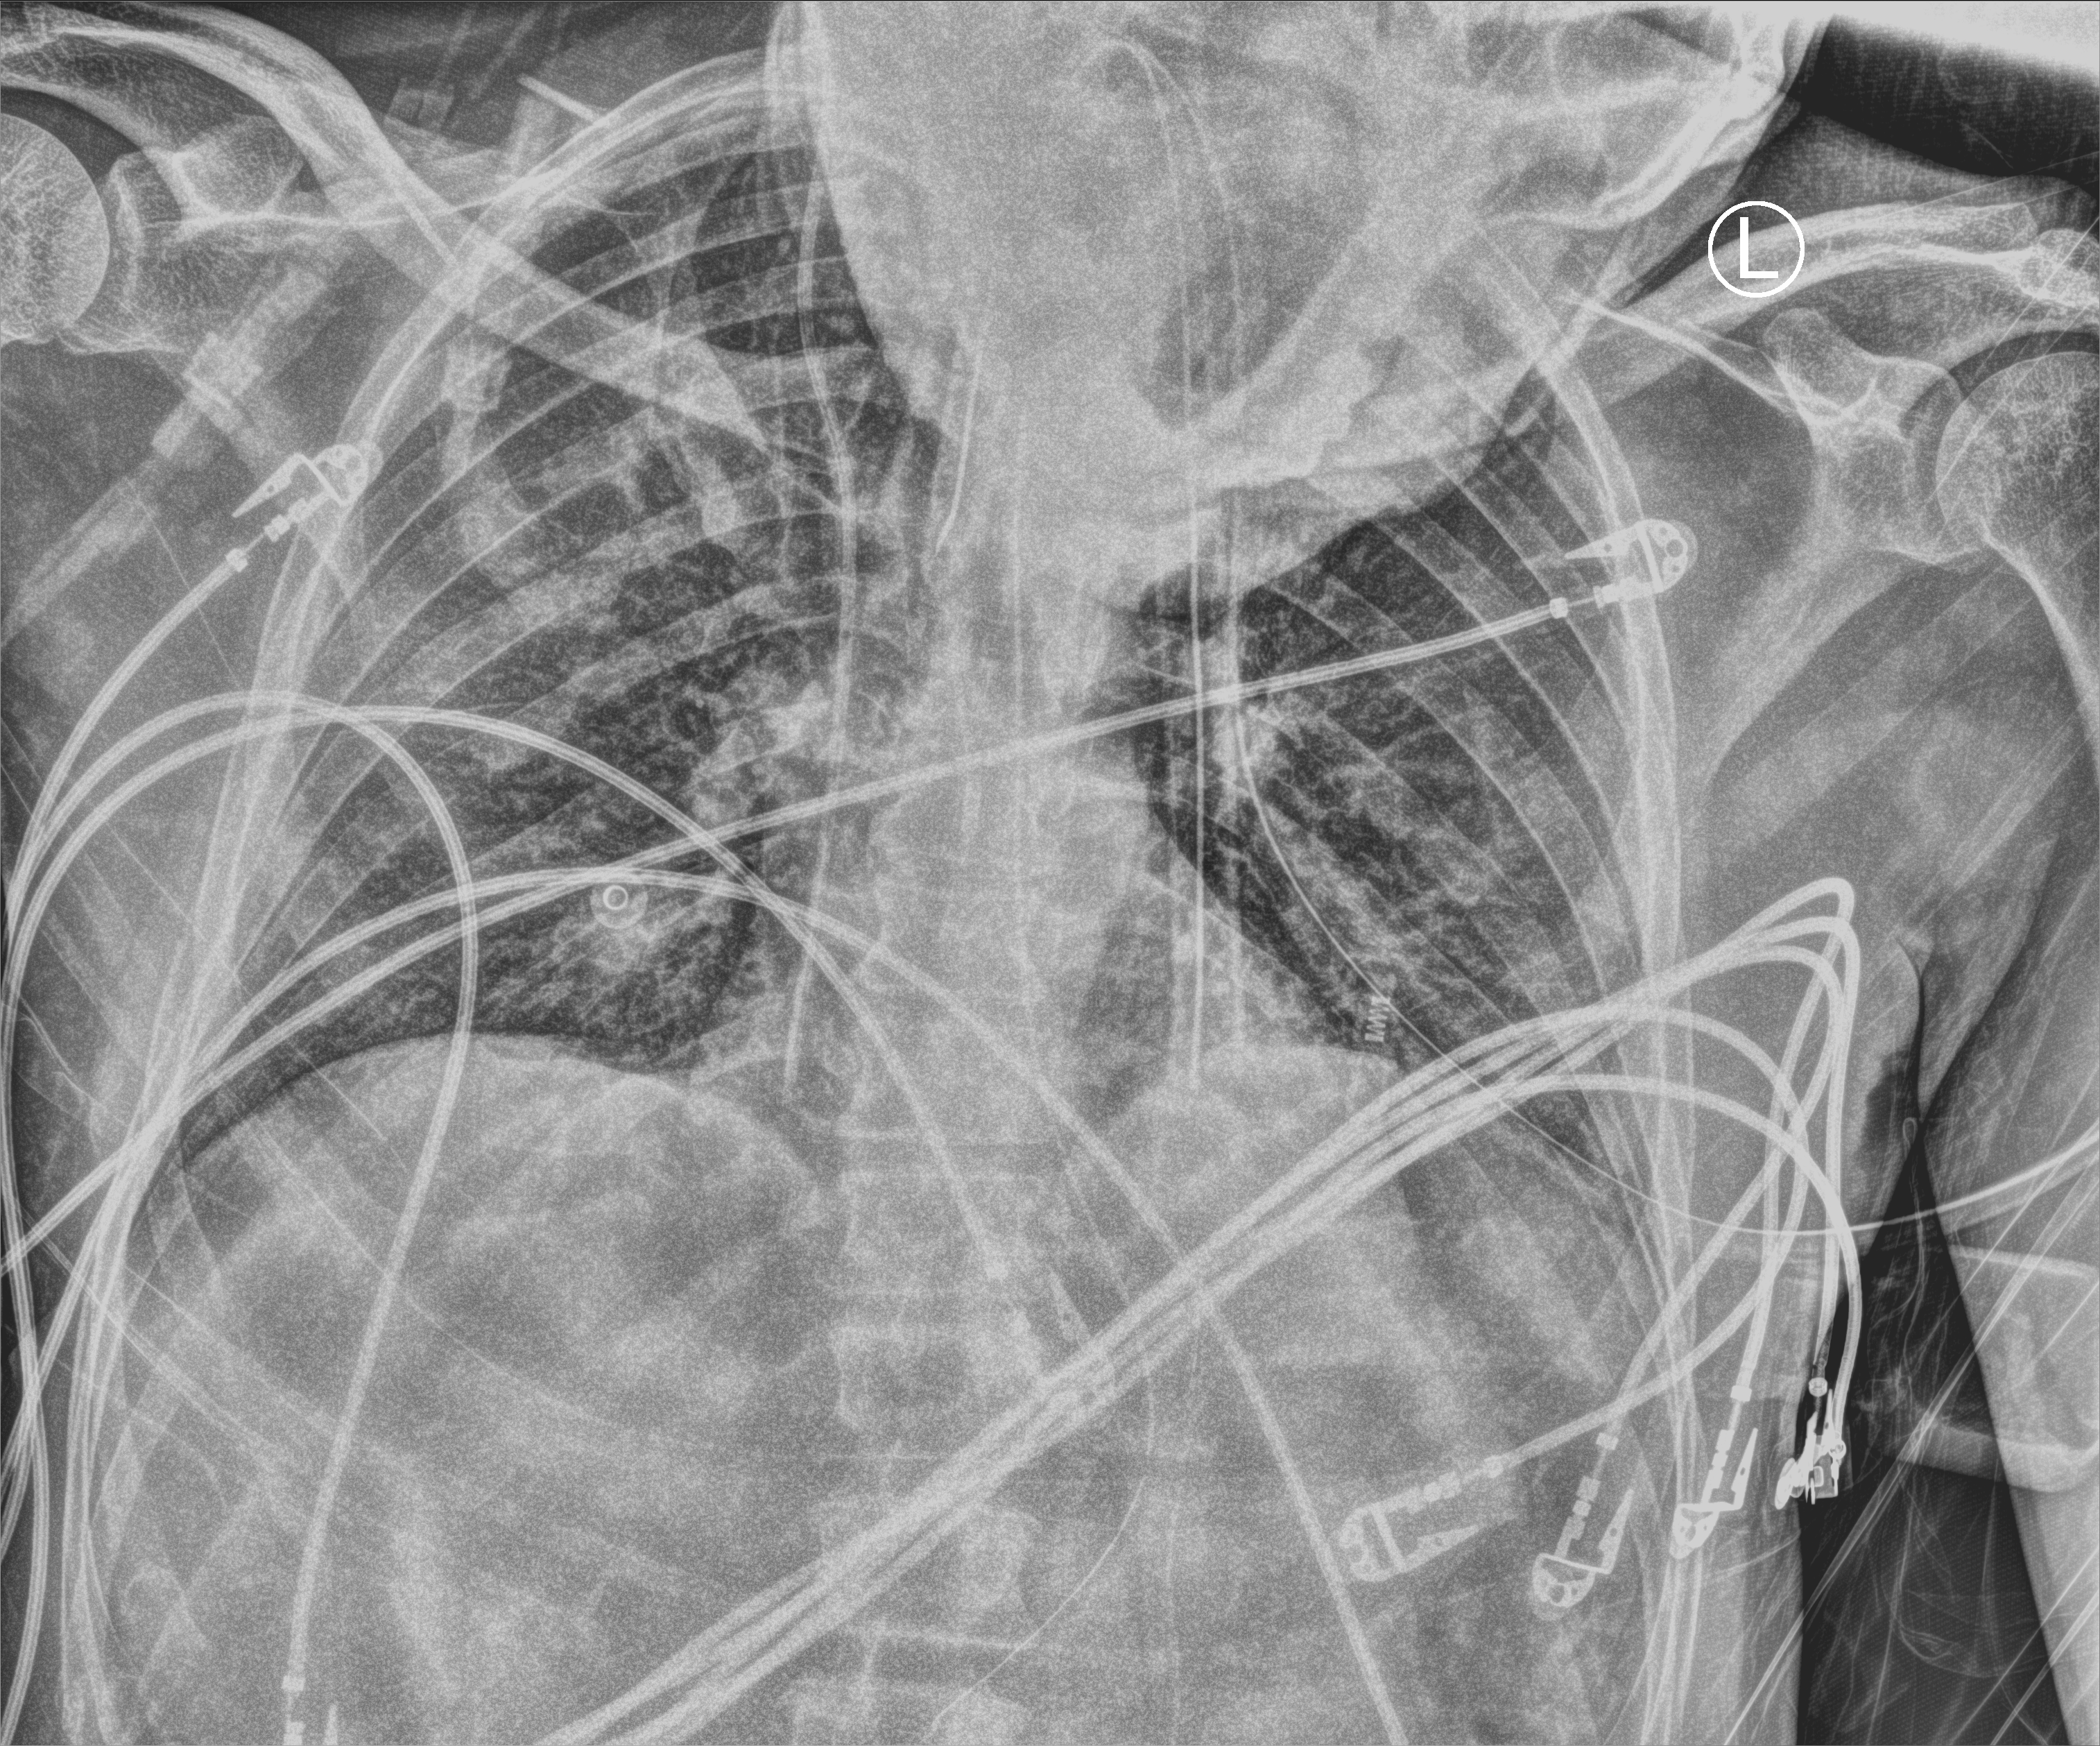
Chest X-ray (portable), anteroposterior (AP) projection. Patient hospitalised with COVID-19; male, aged 18–59 years.
From the hospital-stay record, not from the radiograph (when in the stay this image was taken is not recorded): mechanically ventilated during this hospital stay: yes.